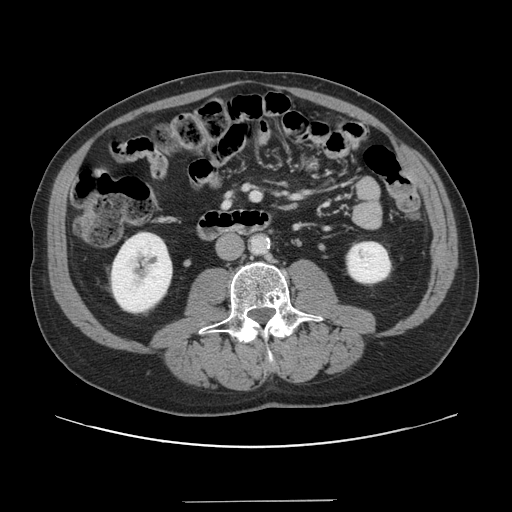
Contrast-enhanced abdominal CT, one axial slice. Intravenous contrast given. Soft-tissue window (W 400 / L 40 HU). 2.5 mm slice thickness. 512 × 512 image matrix, field of view 399 × 399 mm. Male patient, age 63 years. Case-level facts recorded for this patient, not image findings: diagnosis: colorectal cancer liver metastases, imaged before liver resection; multiple liver metastases: no; largest metastasis: 2.1 cm.
Outlined on this slice (manually delineated by an expert):
- portal vein (with intrahepatic branches): bounding box <252,193,258,197> (left, top, right, bottom; pixels)